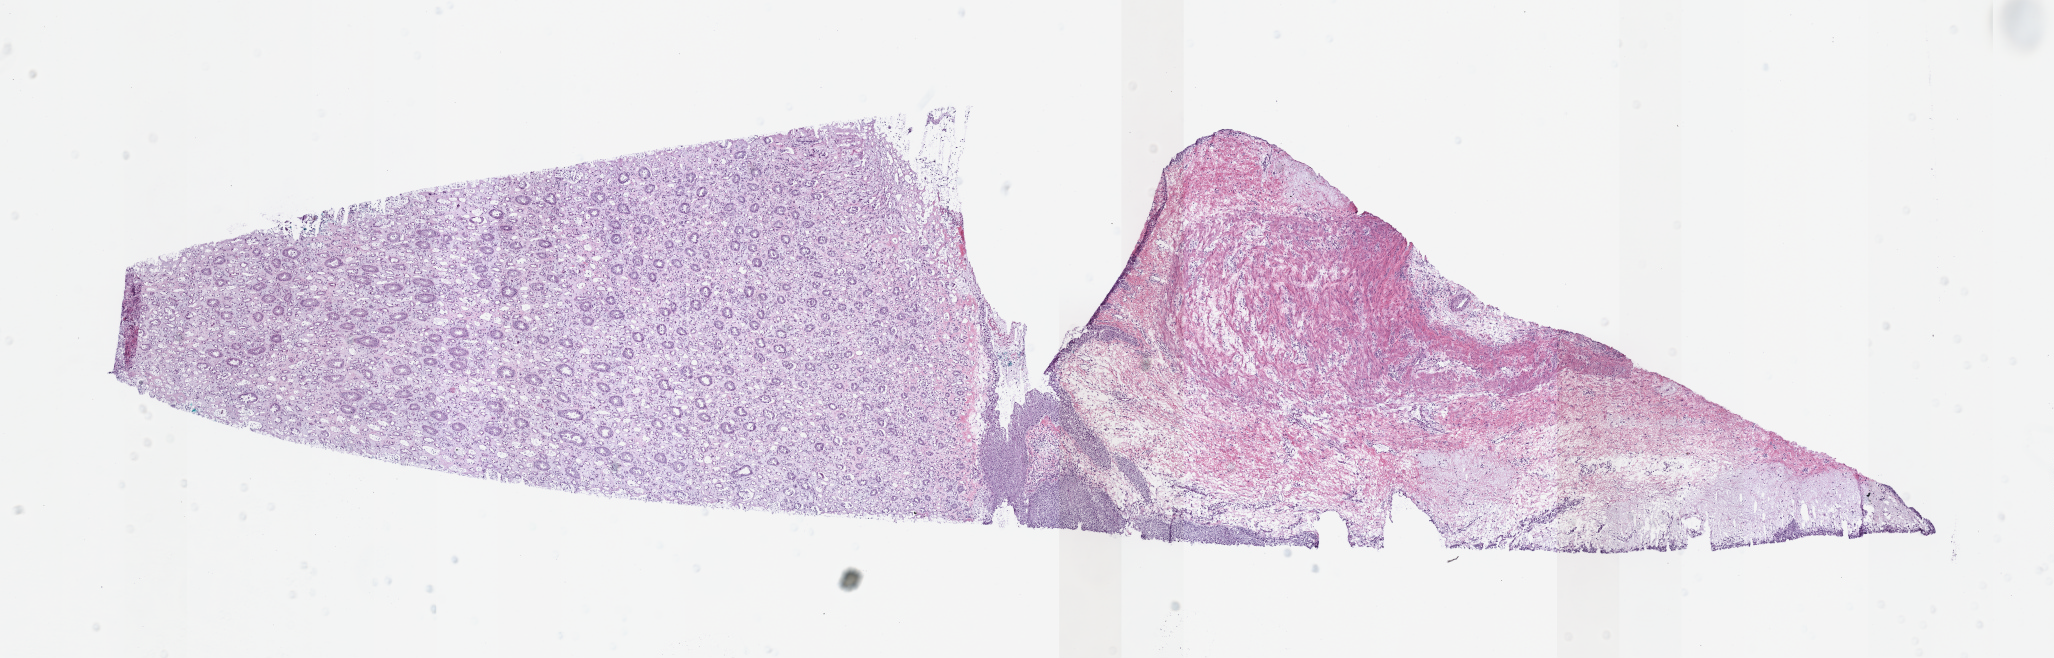
Whole-slide histology image, Hematoxylin and eosin (H&E) stained — shown as a low-resolution overview of the whole scanned area (about 16.2 x 5.2 mm). Frozen section. Solid tissue normal (non-tumour tissue) sample from the kidney. Female patient; age at initial diagnosis 41 years.
This section: solid tissue normal sample (biorepository sample class). Patient diagnosis: Clear cell adenocarcinoma, NOS.